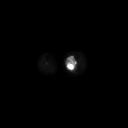
FDG PET of an extremity soft-tissue mass (from a PET/CT study), one axial slice. Slice 143 of 223 in the series (ordered by position). 3.27 mm slice thickness. 128 × 128 image matrix, field of view 700 × 700 mm. Female patient, age 70 years. From the clinical record (not read from this slice): histological type: extraskeletal high grade osteogenic sarcoma; grade: high; site of the primary tumour: left calf.
Structures marked on this image (expert contour drawn on MRI and transferred to this co-registered scan by the dataset authors):
- gross tumour volume (mass): bounding box (x1, y1, x2, y2) in pixels: (66, 57, 77, 70)